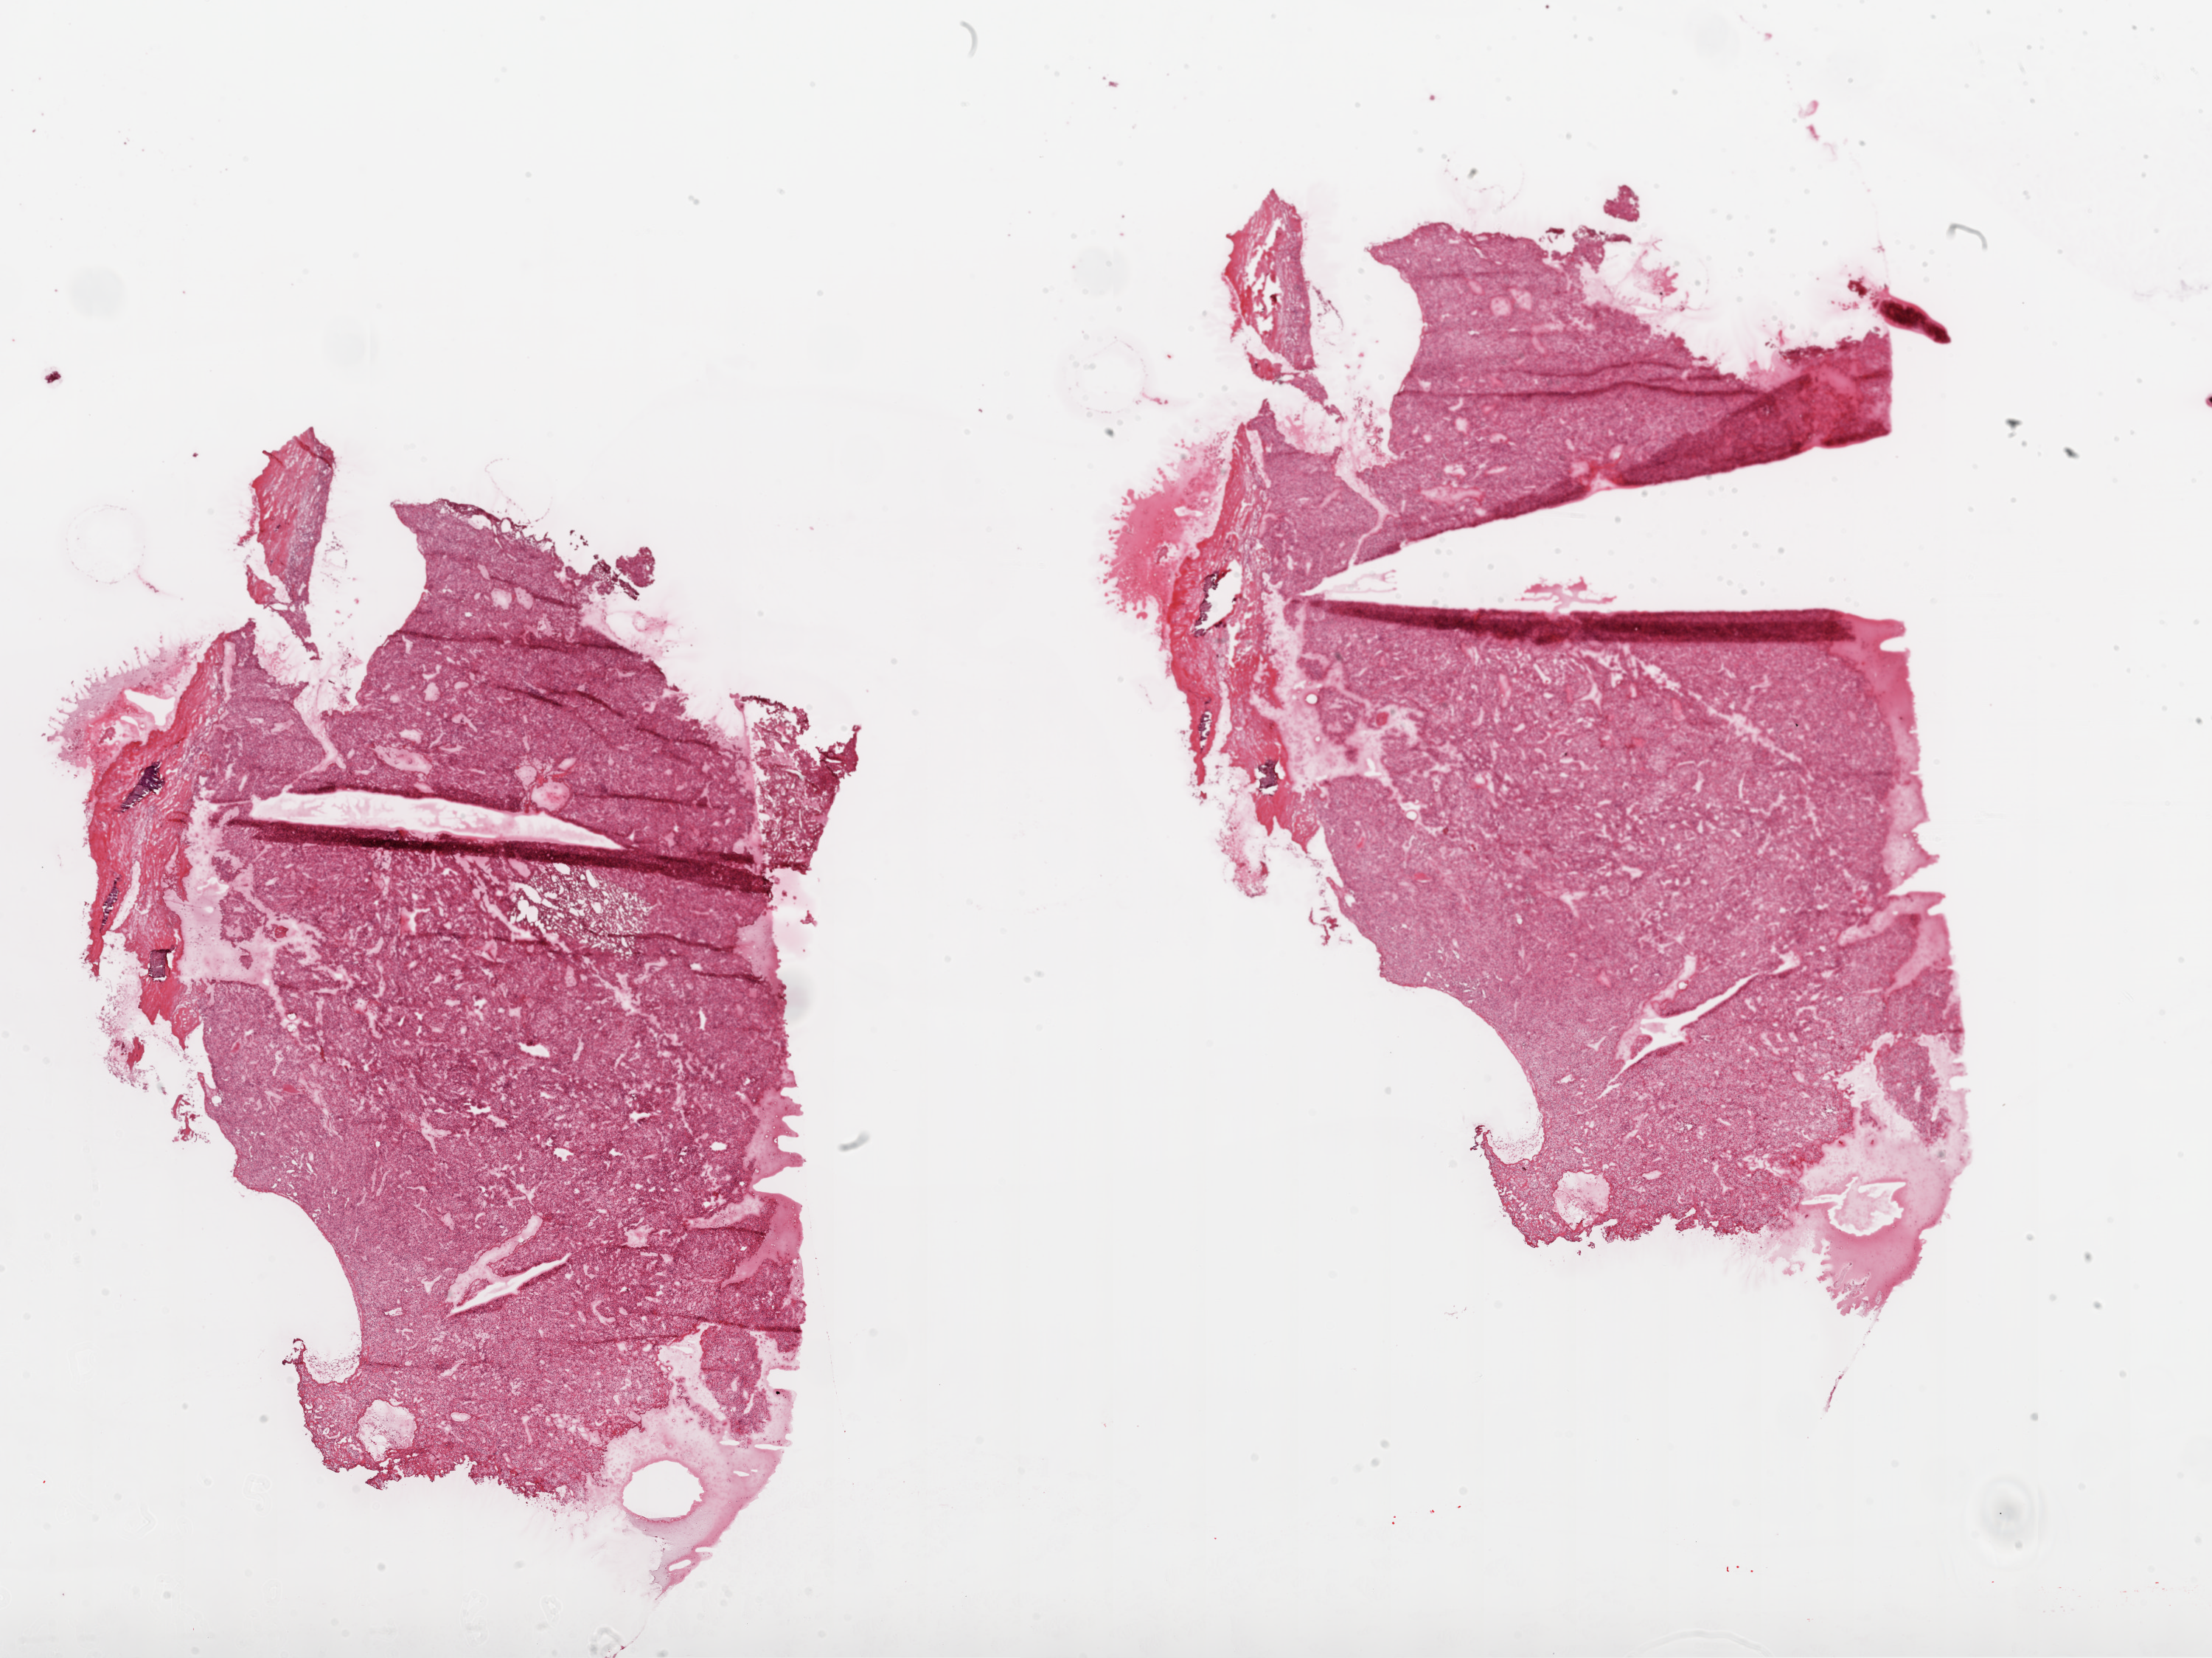
Hematoxylin and eosin (H&E) stained whole-slide image — shown as a low-resolution overview of the whole scanned area (about 24.1 x 18.0 mm, slide scanned at 20x); frozen section from the top of the tissue portion; kidney, primary tumour sample. Male, age 66 years at initial diagnosis. Histologic grade: G4 (undifferentiated). Pathologist review of this section (percent, as recorded): tumour cells 90%, tumour nuclei 85%, normal cells 0%, stromal cells 10%, necrosis 0%.
Diagnosis: Clear cell adenocarcinoma, NOS. AJCC pathologic stage: I.